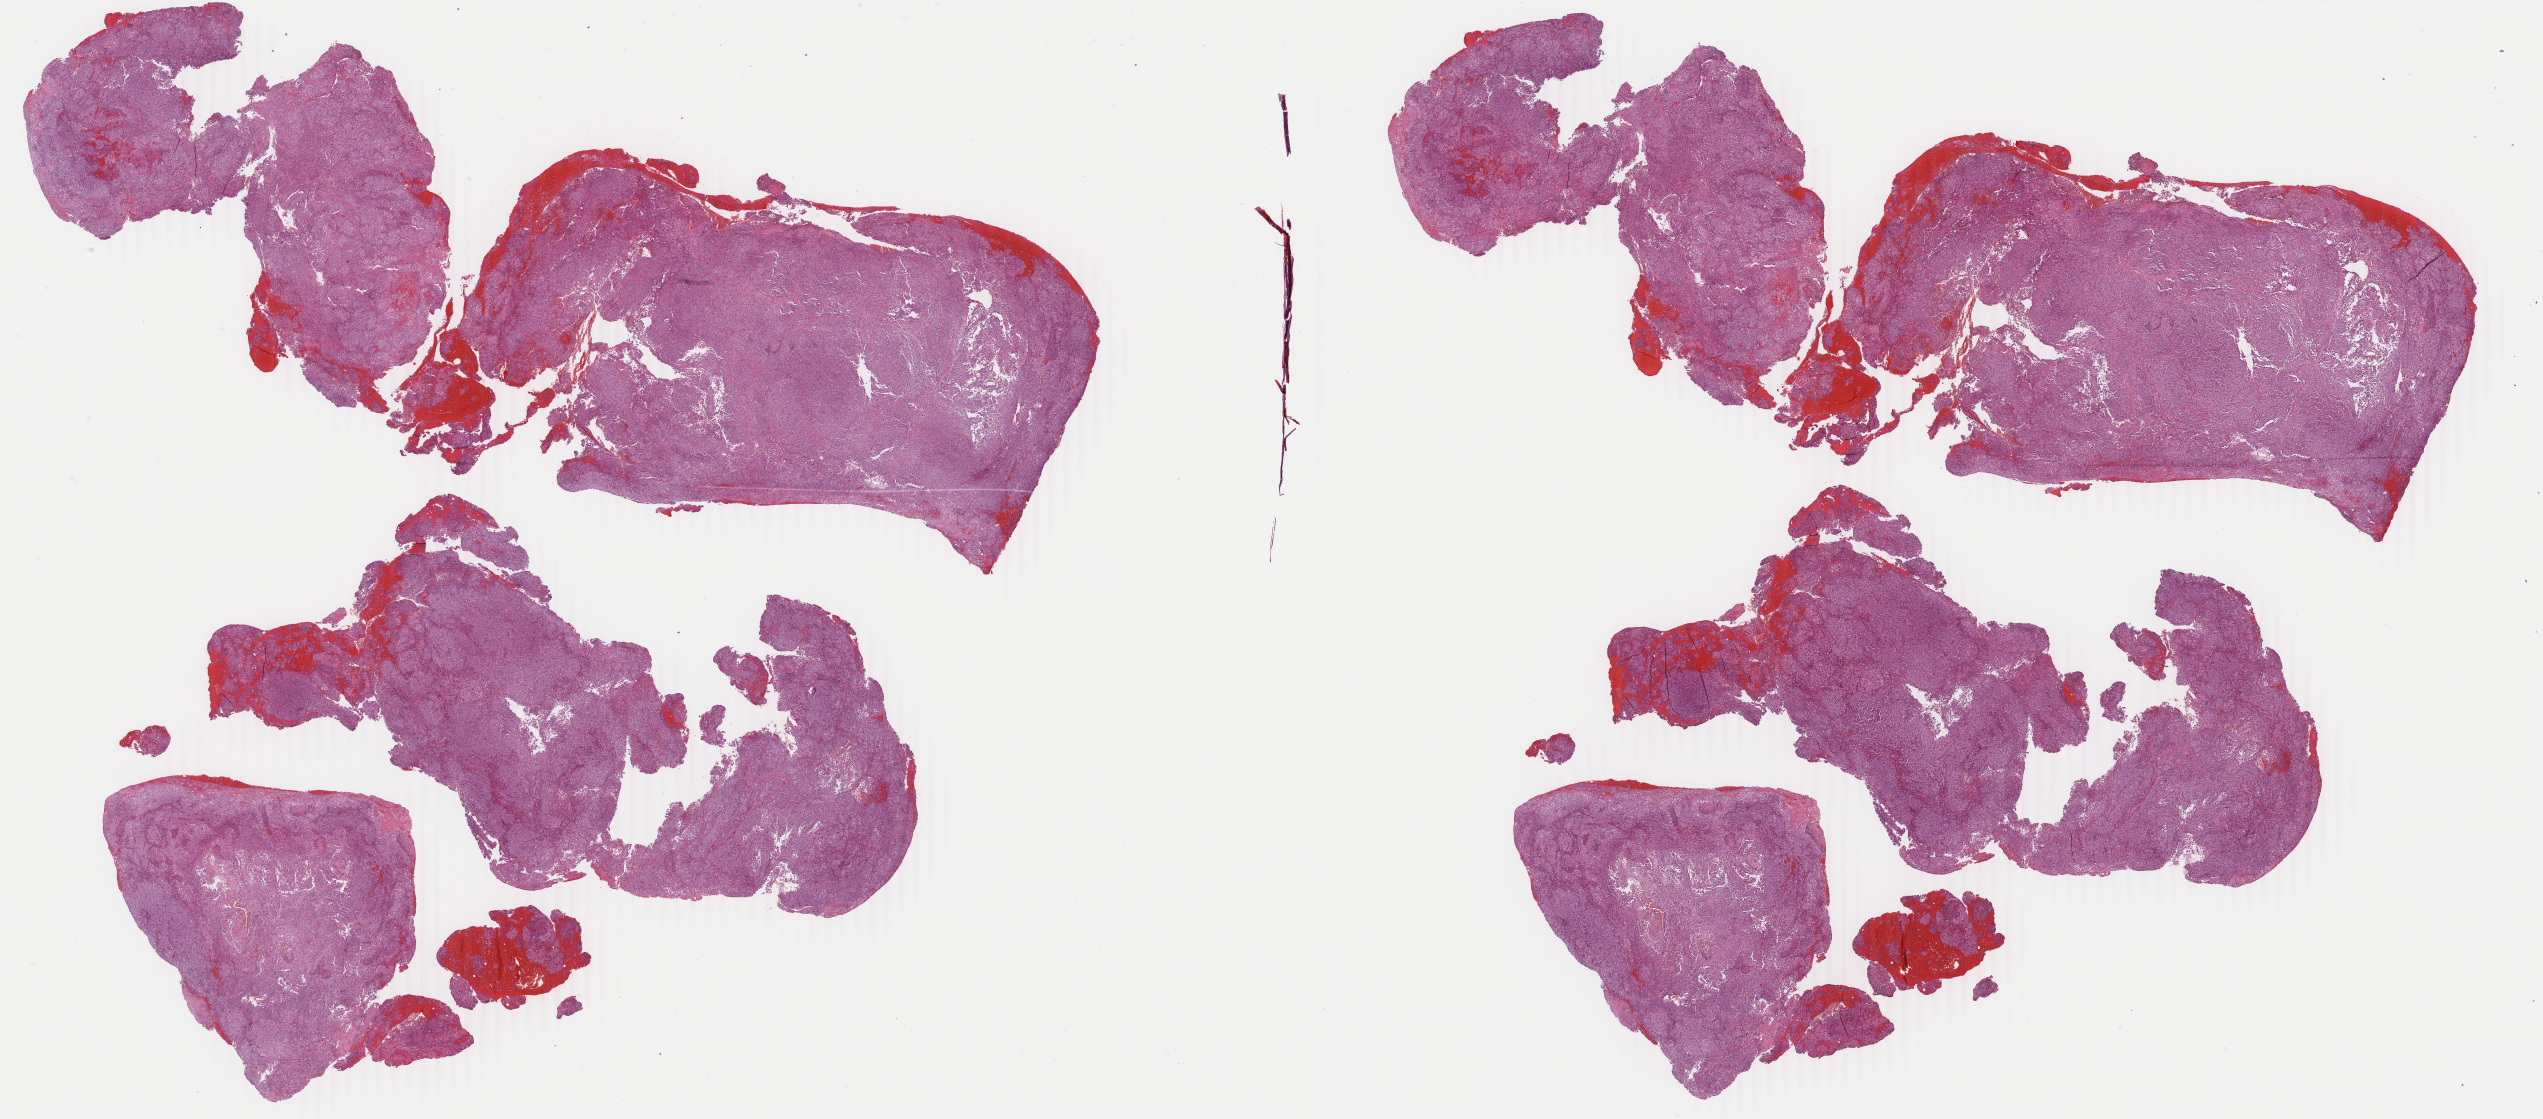
Digitized Hematoxylin and eosin (H&E) stained tissue section (whole slide), whole scanned area (about 40.5 x 17.8 mm) shown as a low-resolution overview, formalin-fixed paraffin-embedded (FFPE) diagnostic section, sample: primary tumour, mesothelium. Female patient; age at initial diagnosis 56 years.
AJCC pathologic stage: III (7th edition). Laterality: right. Histologic diagnosis: Epithelioid mesothelioma, malignant (pleura, NOS).